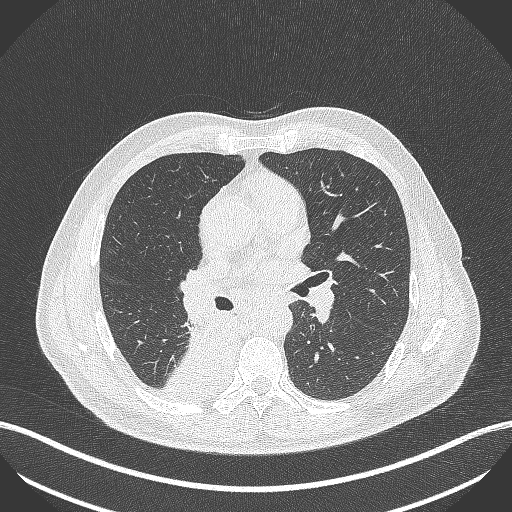
Chest CT, one axial slice; slice 260 of 451 in the series (ordered by position); 100 kVp; lung window (W 1500 / L -600 HU); 1 mm slice thickness; 512 × 512 image matrix, field of view 400 × 400 mm. Patient: male, 61 years. Case-level facts recorded for this patient, not image findings: clinical TNM (as recorded): T1 N0 M0; histopathological grade: G3.
Structures marked on this image (bounding box drawn by a radiologist):
- lung tumour (recorded histology: small cell carcinoma): bounding box <162,303,238,402> (left, top, right, bottom; pixels)